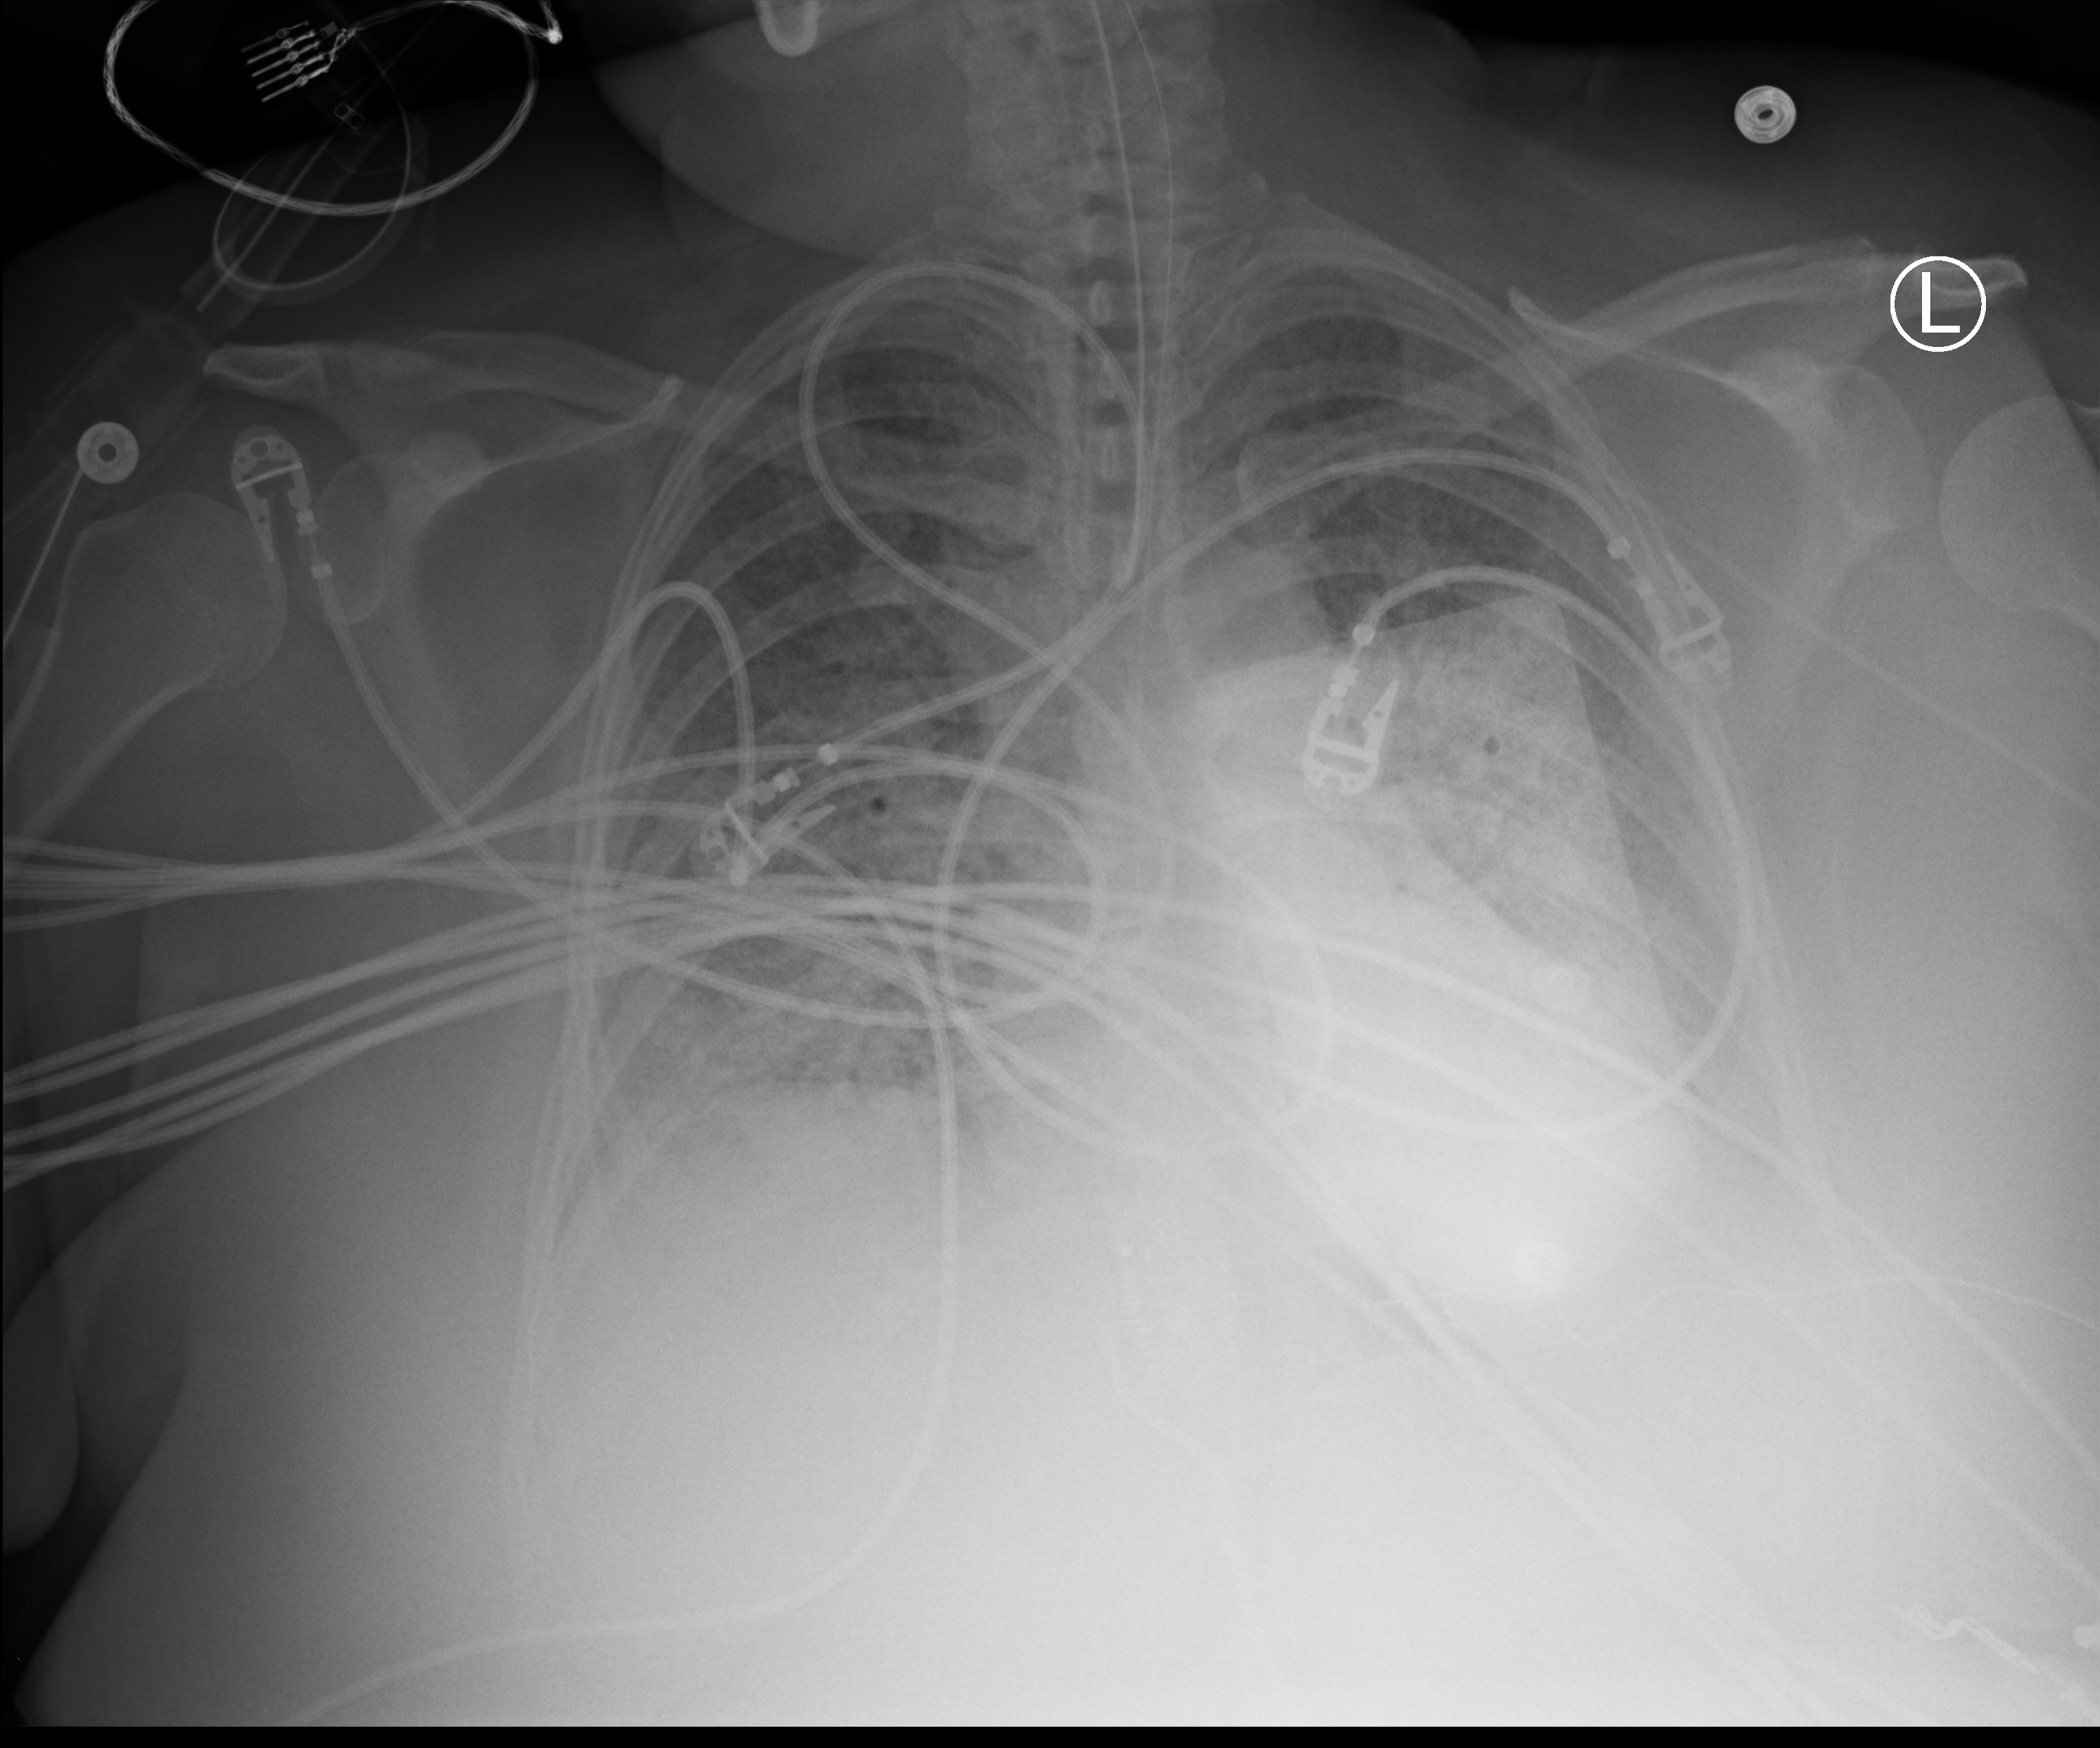
Bedside chest radiograph (computed radiography); anteroposterior (AP) projection. Female patient hospitalised with COVID-19, age 18–59 years.
Hospital-stay facts (about this admission, not read from this image; timing relative to this image not recorded):
- smoking status (admission record): never
- length of hospital stay: 95 days
- mechanically ventilated during this hospital stay: yes